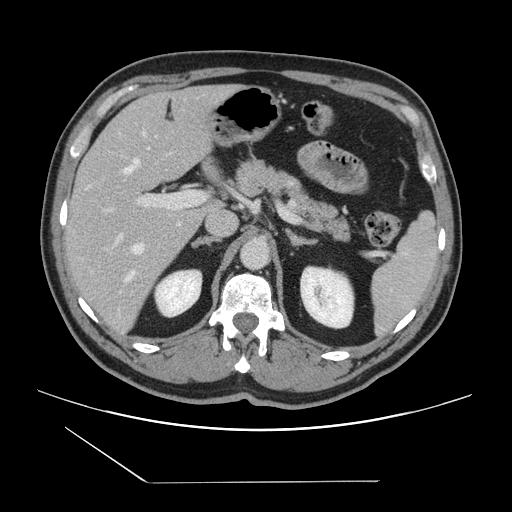
Contrast-enhanced abdominal CT, one axial slice. Position 86 of 157 along the scan axis. Intravenous contrast given. Soft-tissue window (W 400 / L 40 HU). 2.5 mm slice thickness. 512 × 512 image matrix, field of view 407 × 407 mm. Male patient, age 61 years. Case-level facts recorded for this patient, not image findings: diagnosis: colorectal cancer liver metastases, imaged before liver resection; multiple liver metastases: yes; largest metastasis: 5.5 cm; disease in both lobes: yes.
Outlined on this slice (expert manual segmentation):
- hepatic veins: box from (x=122, y=131) to (x=146, y=279) px
- liver: (x=66, y=85)–(x=233, y=338)
- planned liver remnant (the part of the liver to remain after resection): (x=67, y=85)–(x=232, y=221)
- portal vein (with intrahepatic branches): (x=104, y=190)–(x=205, y=246)